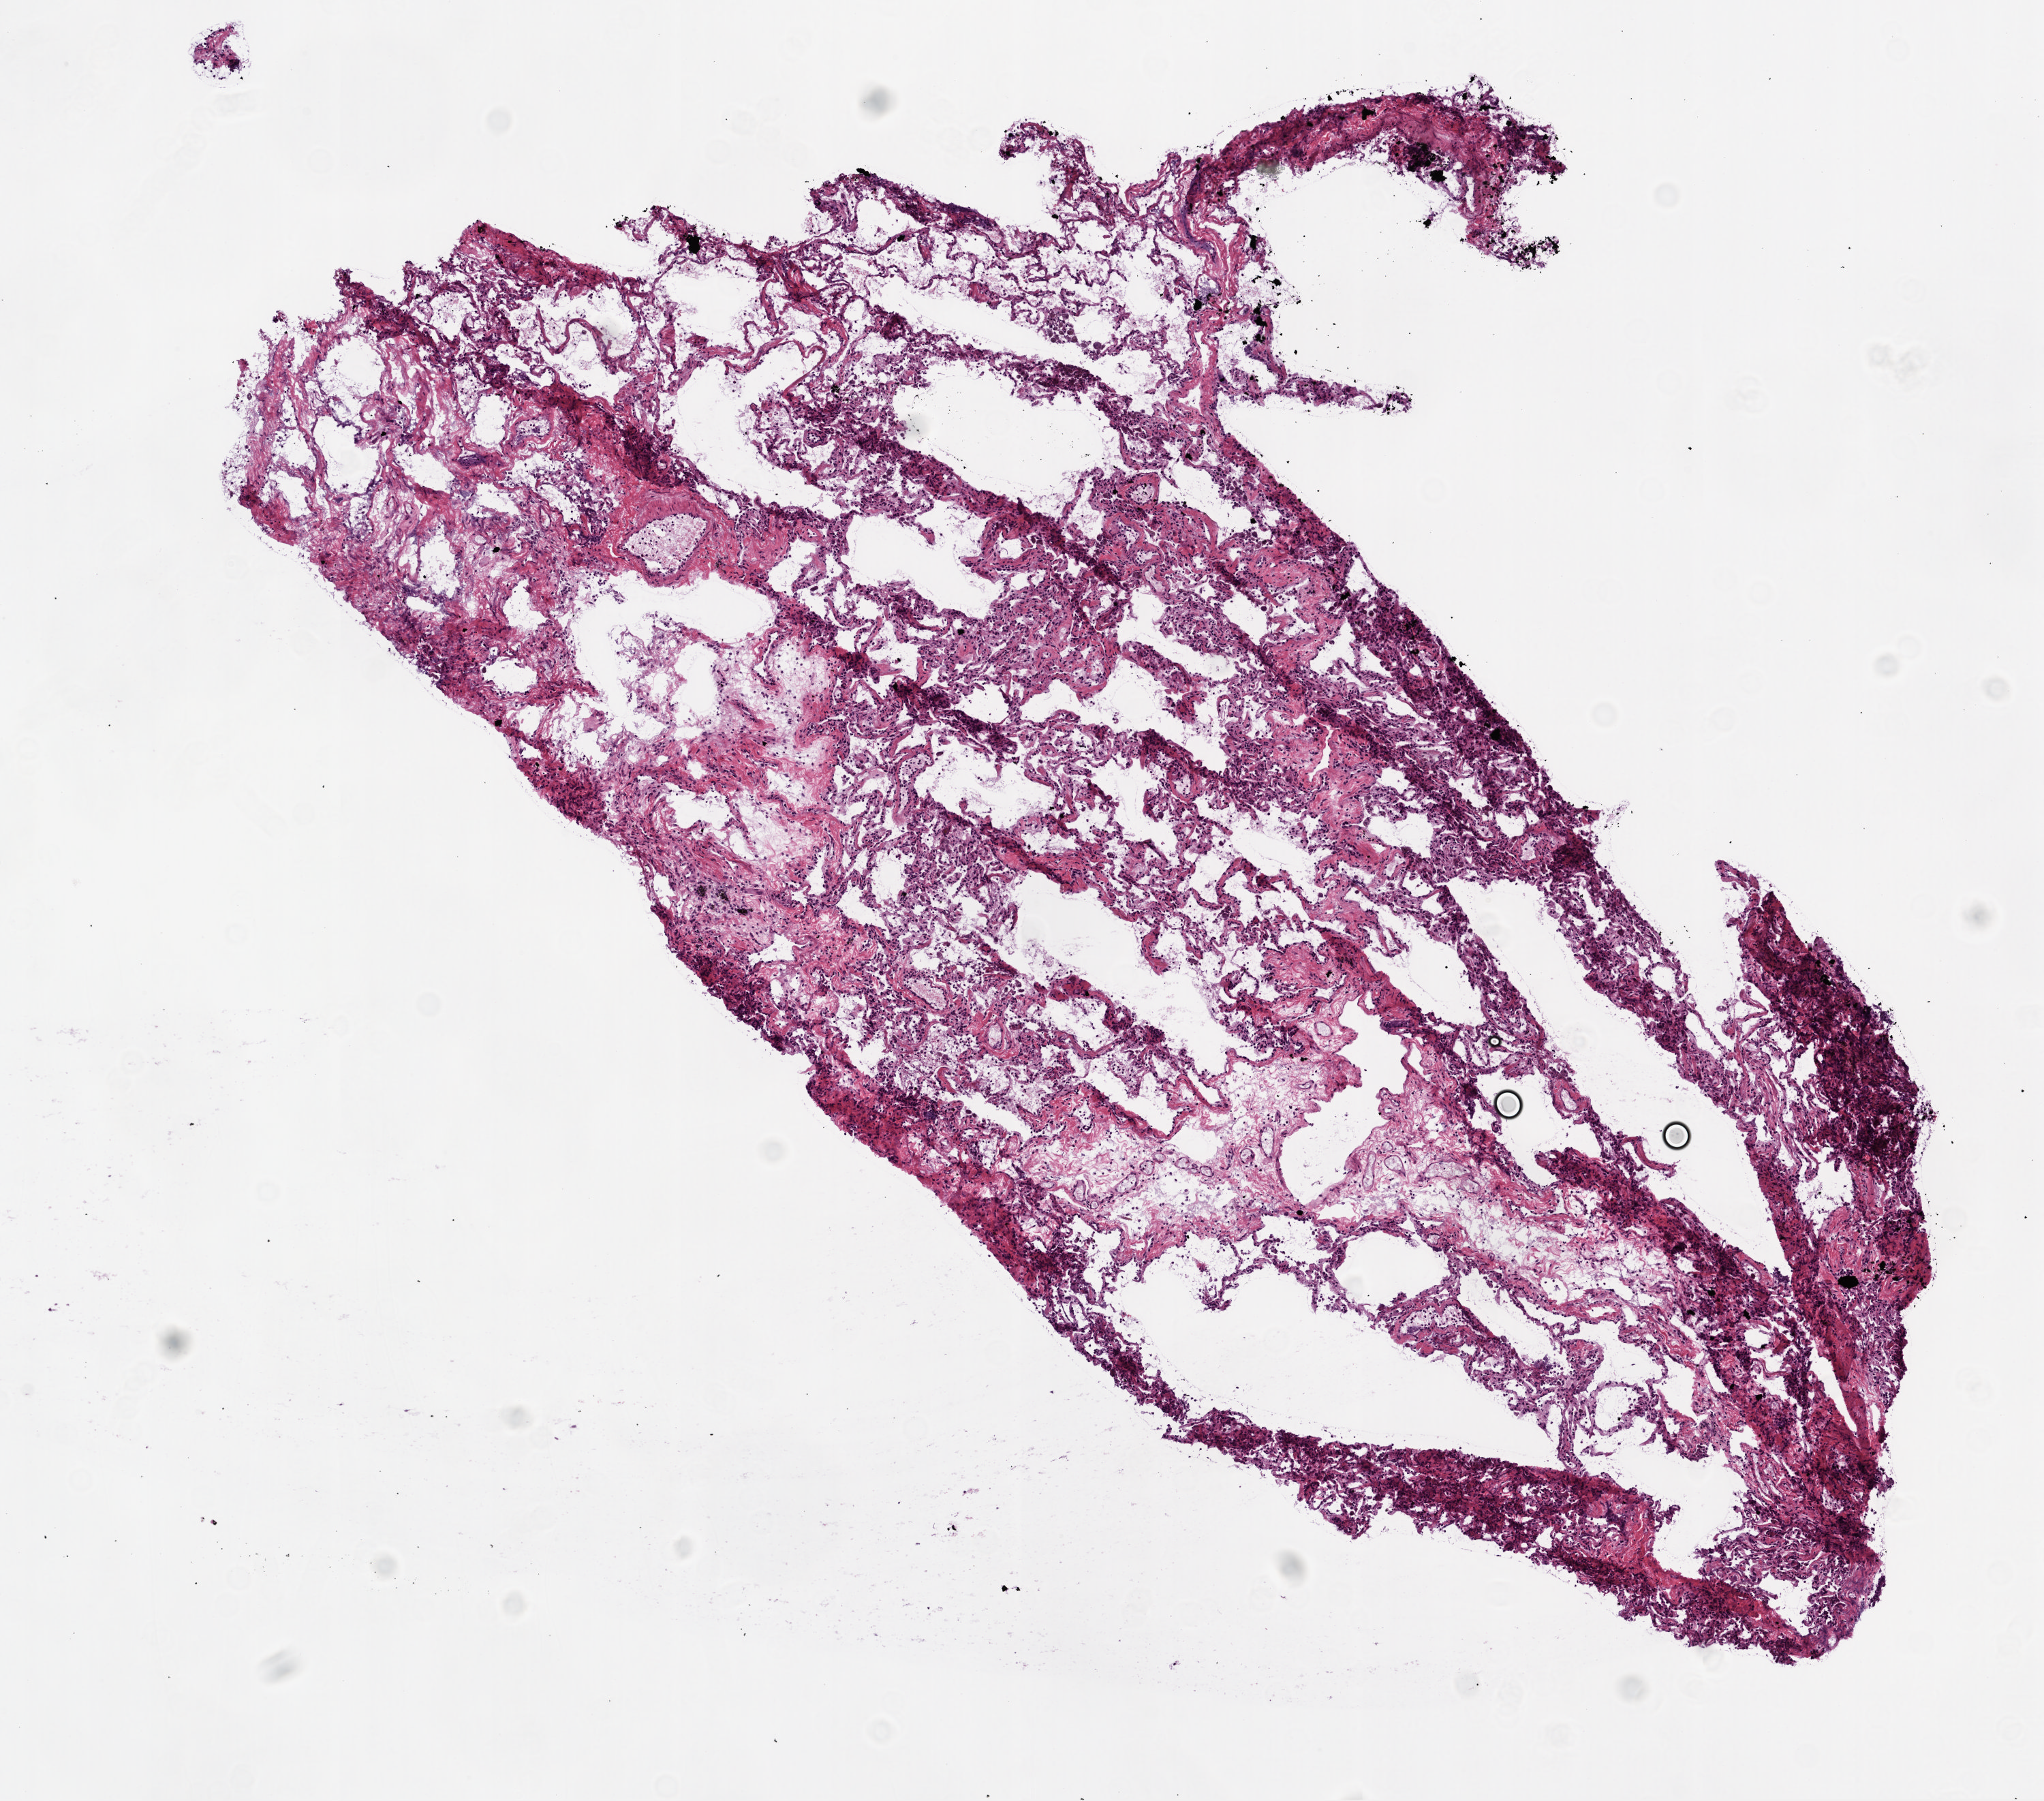
Whole-slide histology image, Hematoxylin and eosin (H&E) stained — whole scanned area (about 6.0 x 5.3 mm, slide scanned at 20x) shown as a low-resolution overview, frozen section from the top of the tissue portion, solid tissue normal (non-tumour tissue) sample from the lung. Patient: female, age at initial diagnosis 60 years.
- this section: solid tissue normal sample (biorepository sample class)
- patient diagnosis: Squamous cell carcinoma, NOS (lower lobe, lung)